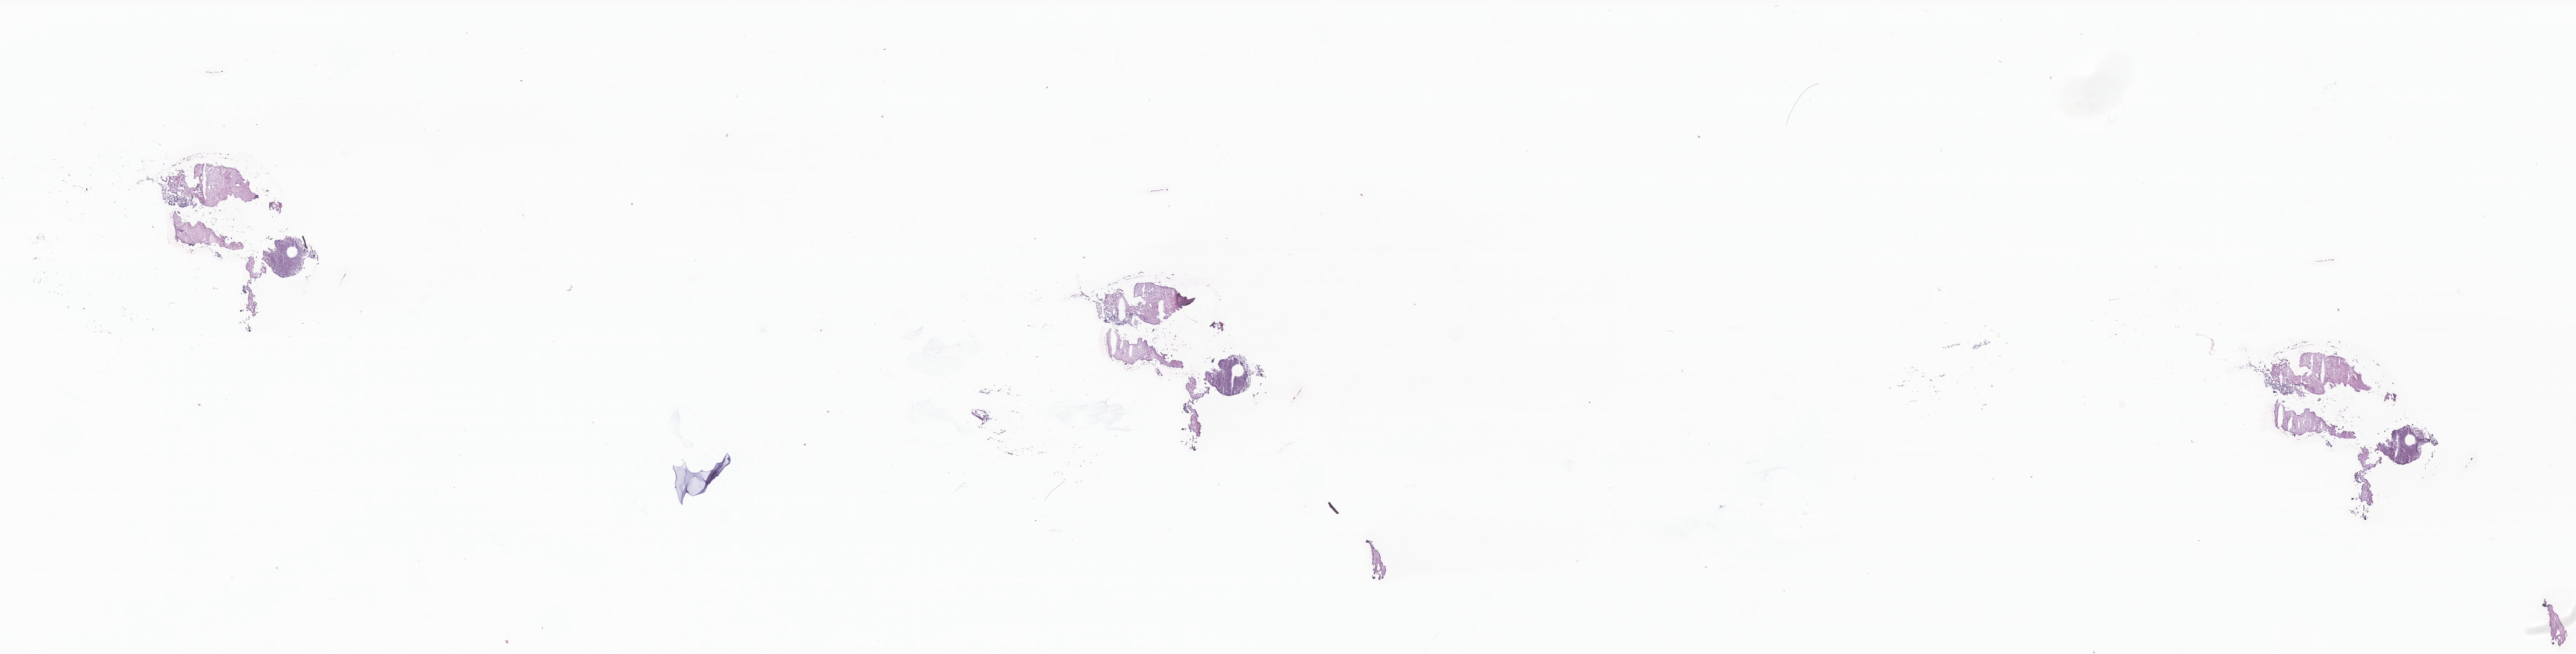
H&E whole-slide image of tumor tissue from the brain, whole scanned area (about 34.3 x 8.7 mm) shown as a low-resolution overview. Cryosection (OCT / tissue freezing medium). Female patient, age 80 months.
- diagnosis (ICD-O-3 morphology term): Medulloblastoma, NOS